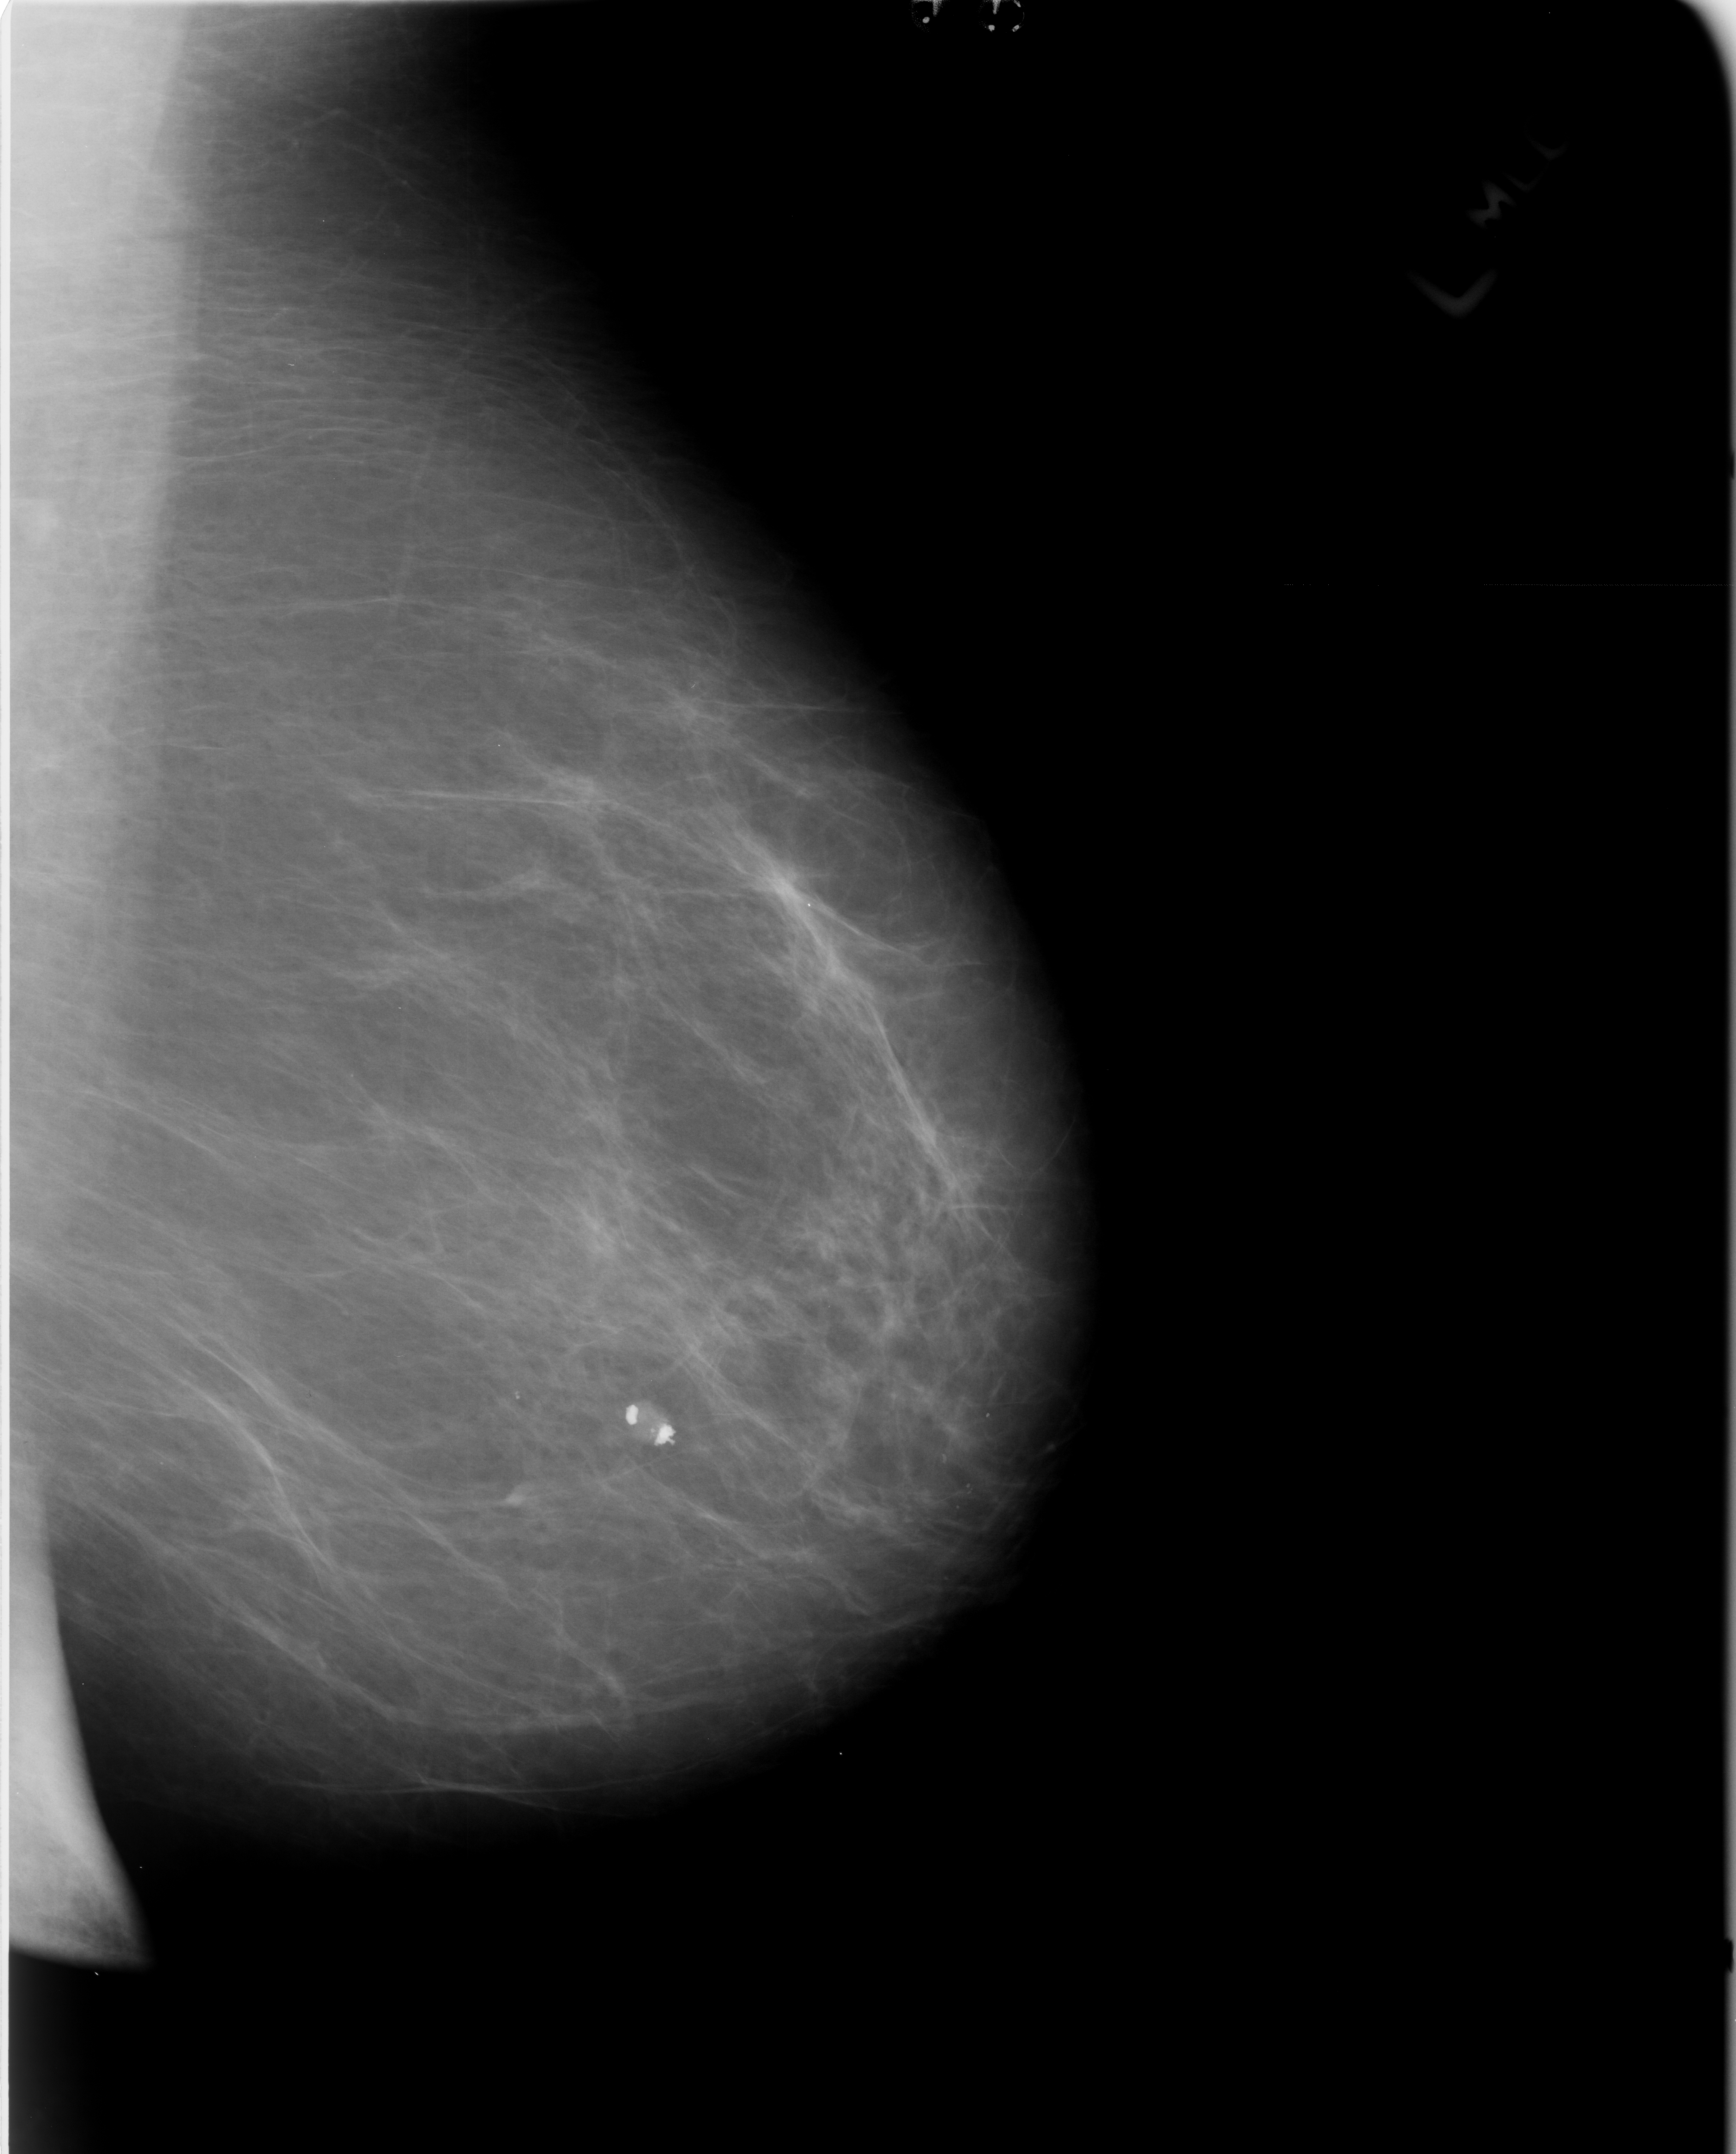
Digitized screen-film mammogram. Left breast. Mediolateral oblique (MLO) view. 1736 × 2154 image matrix.
Expert-marked regions of interest on this image (one box per marked abnormality):
- calcifications, morphology coarse; BI-RADS assessment category 2; benign; no additional work-up was recommended (outcome (as recorded, no biopsy): benign without callback): bounding box [x1, y1, x2, y2] px = [615, 1401, 680, 1449]